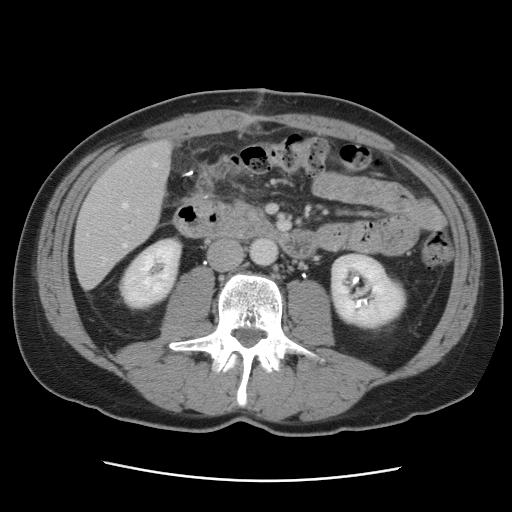
Contrast-enhanced abdominal CT, one axial slice; position 24 of 89 along the scan axis; intravenous contrast given; soft-tissue window (W 400 / L 40 HU); 5 mm slice thickness; 512 × 512 image matrix, field of view 366 × 366 mm. Male patient, age 59 years. Case-level facts recorded for this patient, not image findings: diagnosis: colorectal cancer liver metastases, imaged before liver resection; multiple liver metastases: yes; largest metastasis: 0.6 cm; chemotherapy before resection: no.
Outlined on this slice (manually delineated by an expert):
- hepatic veins: bounding box [x1, y1, x2, y2] px = [102, 162, 158, 265]
- liver: [76, 142, 171, 288]
- planned liver remnant (the part of the liver to remain after resection): [76, 143, 171, 249]
- portal vein (with intrahepatic branches): [125, 226, 128, 230]